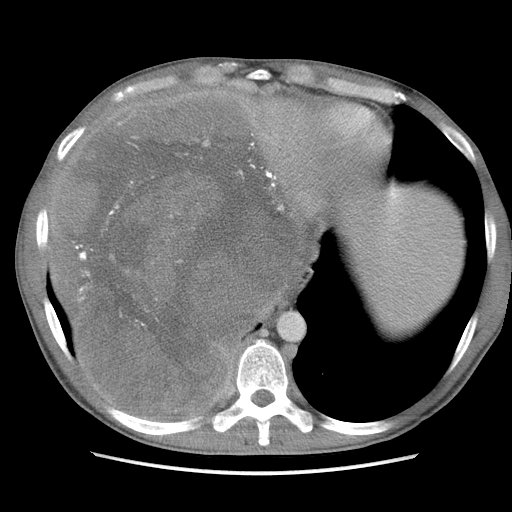
Contrast-enhanced abdominal CT, one axial slice; position 89 of 115 along the scan axis; soft-tissue window (W 400 / L 40 HU); 512 × 512 image matrix, field of view 360 × 360 mm. Male patient. From the clinical record (not read from this slice): diagnosis: adrenocortical carcinoma; tumour side: right adrenal; Ki-67 index: 13 %; stage (as recorded): 3.
Outlined on this slice (semi-automatically segmented with operator editing):
- mass: box from (x=59, y=97) to (x=297, y=414) px